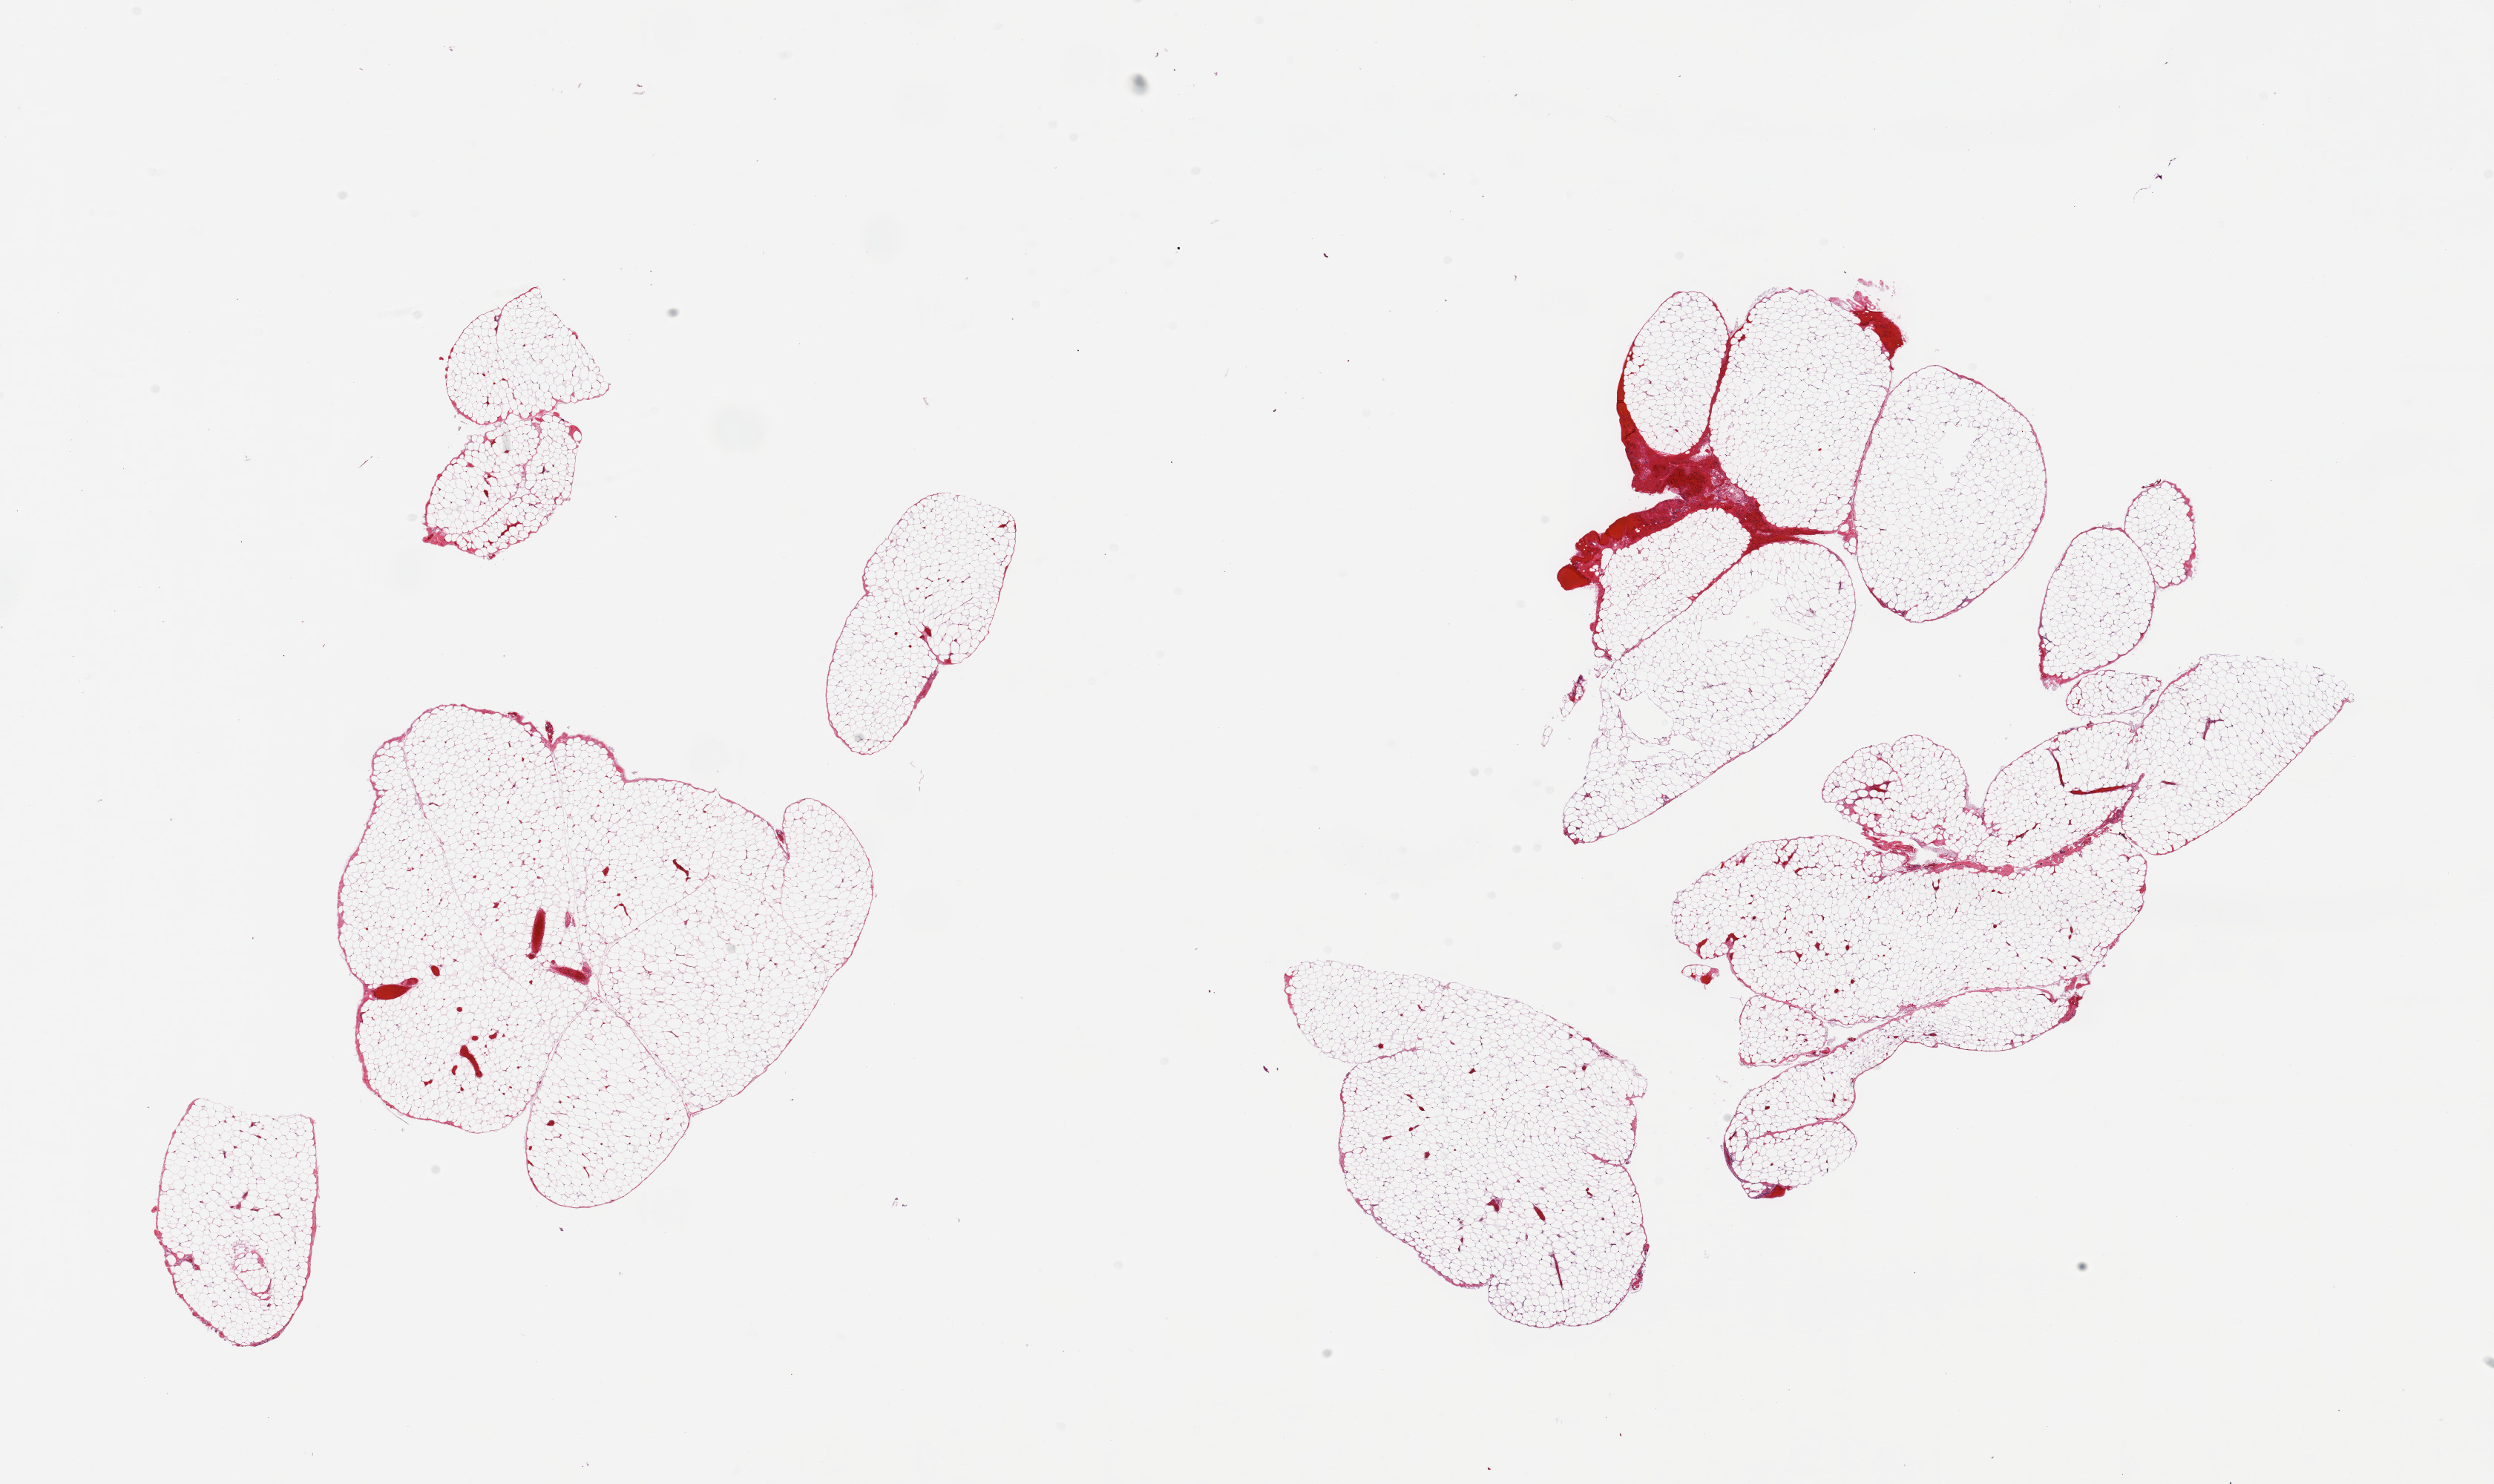
Haematoxylin and eosin whole-slide image, a low-resolution overview of the entire scanned area, about 26.6 x 15.8 mm (acquisition: 20x scan), PAXgene-fixed paraffin-embedded (PFPE) section, sampled site (target tissue): omentum, tissue donor sample. Donor: male.
- pathologist's review note for this sample: 2 pieces, ~5-10% fascia/vascular elements